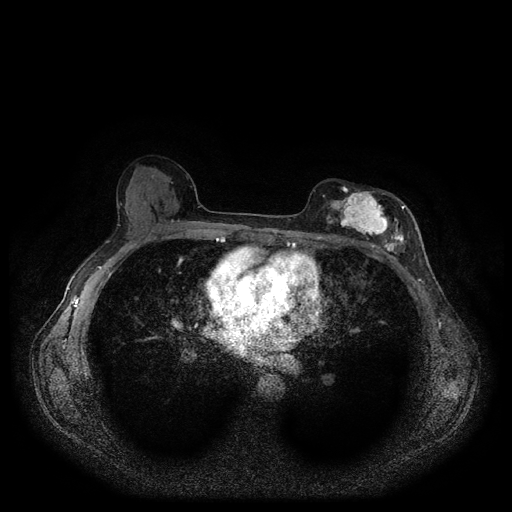
Breast MRI (dynamic contrast-enhanced, multi-phase), one axial slice; position 58 of 116 along the scan axis; dynamic contrast-enhanced series, time point 2 of 5 at this slice position (early post-contrast); 1.5 T; TE 2.6 ms, TR 5.3 ms; 2 mm slice thickness; 512 × 512 image matrix, field of view 350 × 350 mm. Female patient, age 51 years.
Outlined on this slice (semi-automatically segmented with operator editing):
- breast lesion (labelled 'tumour' in the annotation; benign lesions carry a separate 'benign' label): bounding box <317,183,406,257> (left, top, right, bottom; pixels)